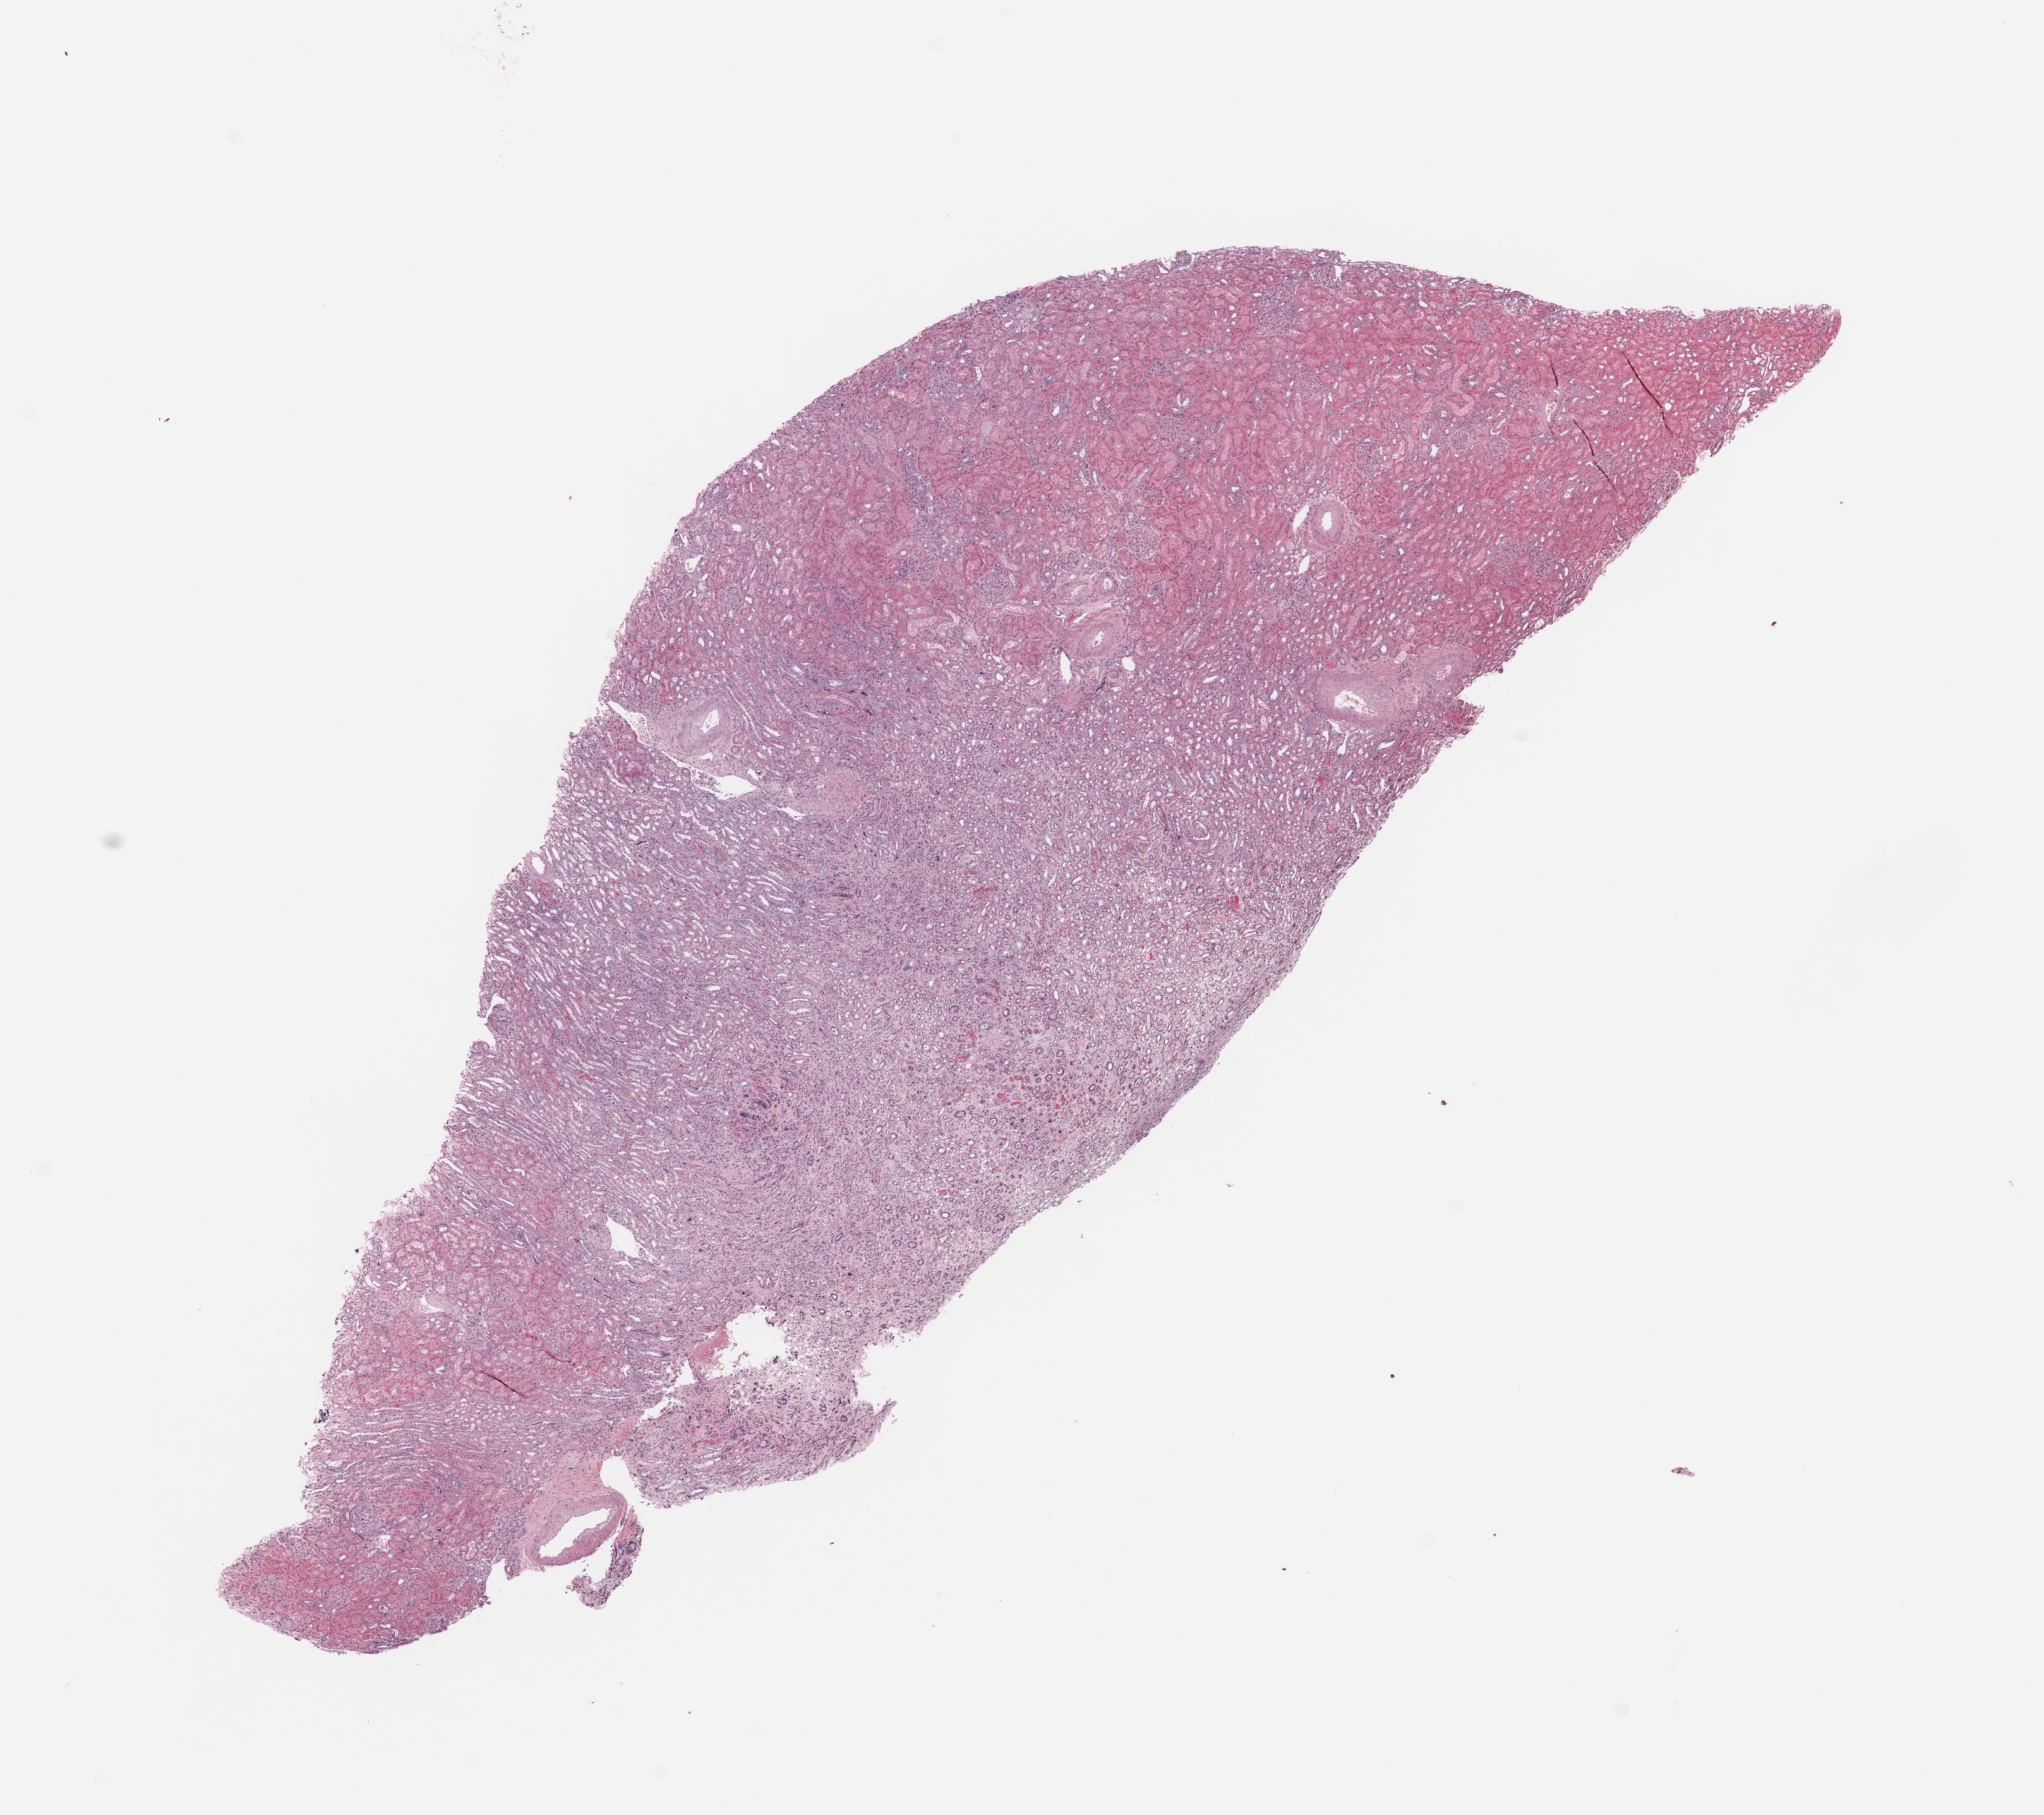
Digitized Hematoxylin and eosin (H&E) stained tissue section (whole slide), low-resolution overview of the scanned area, about 12.8 x 11.4 mm, normal (non-tumour) tissue sample, sampled site: kidney. Patient: male, age 68 years.
This section: normal (non-tumour) tissue from the same patient. Patient diagnosis: Renal cell carcinoma, NOS.